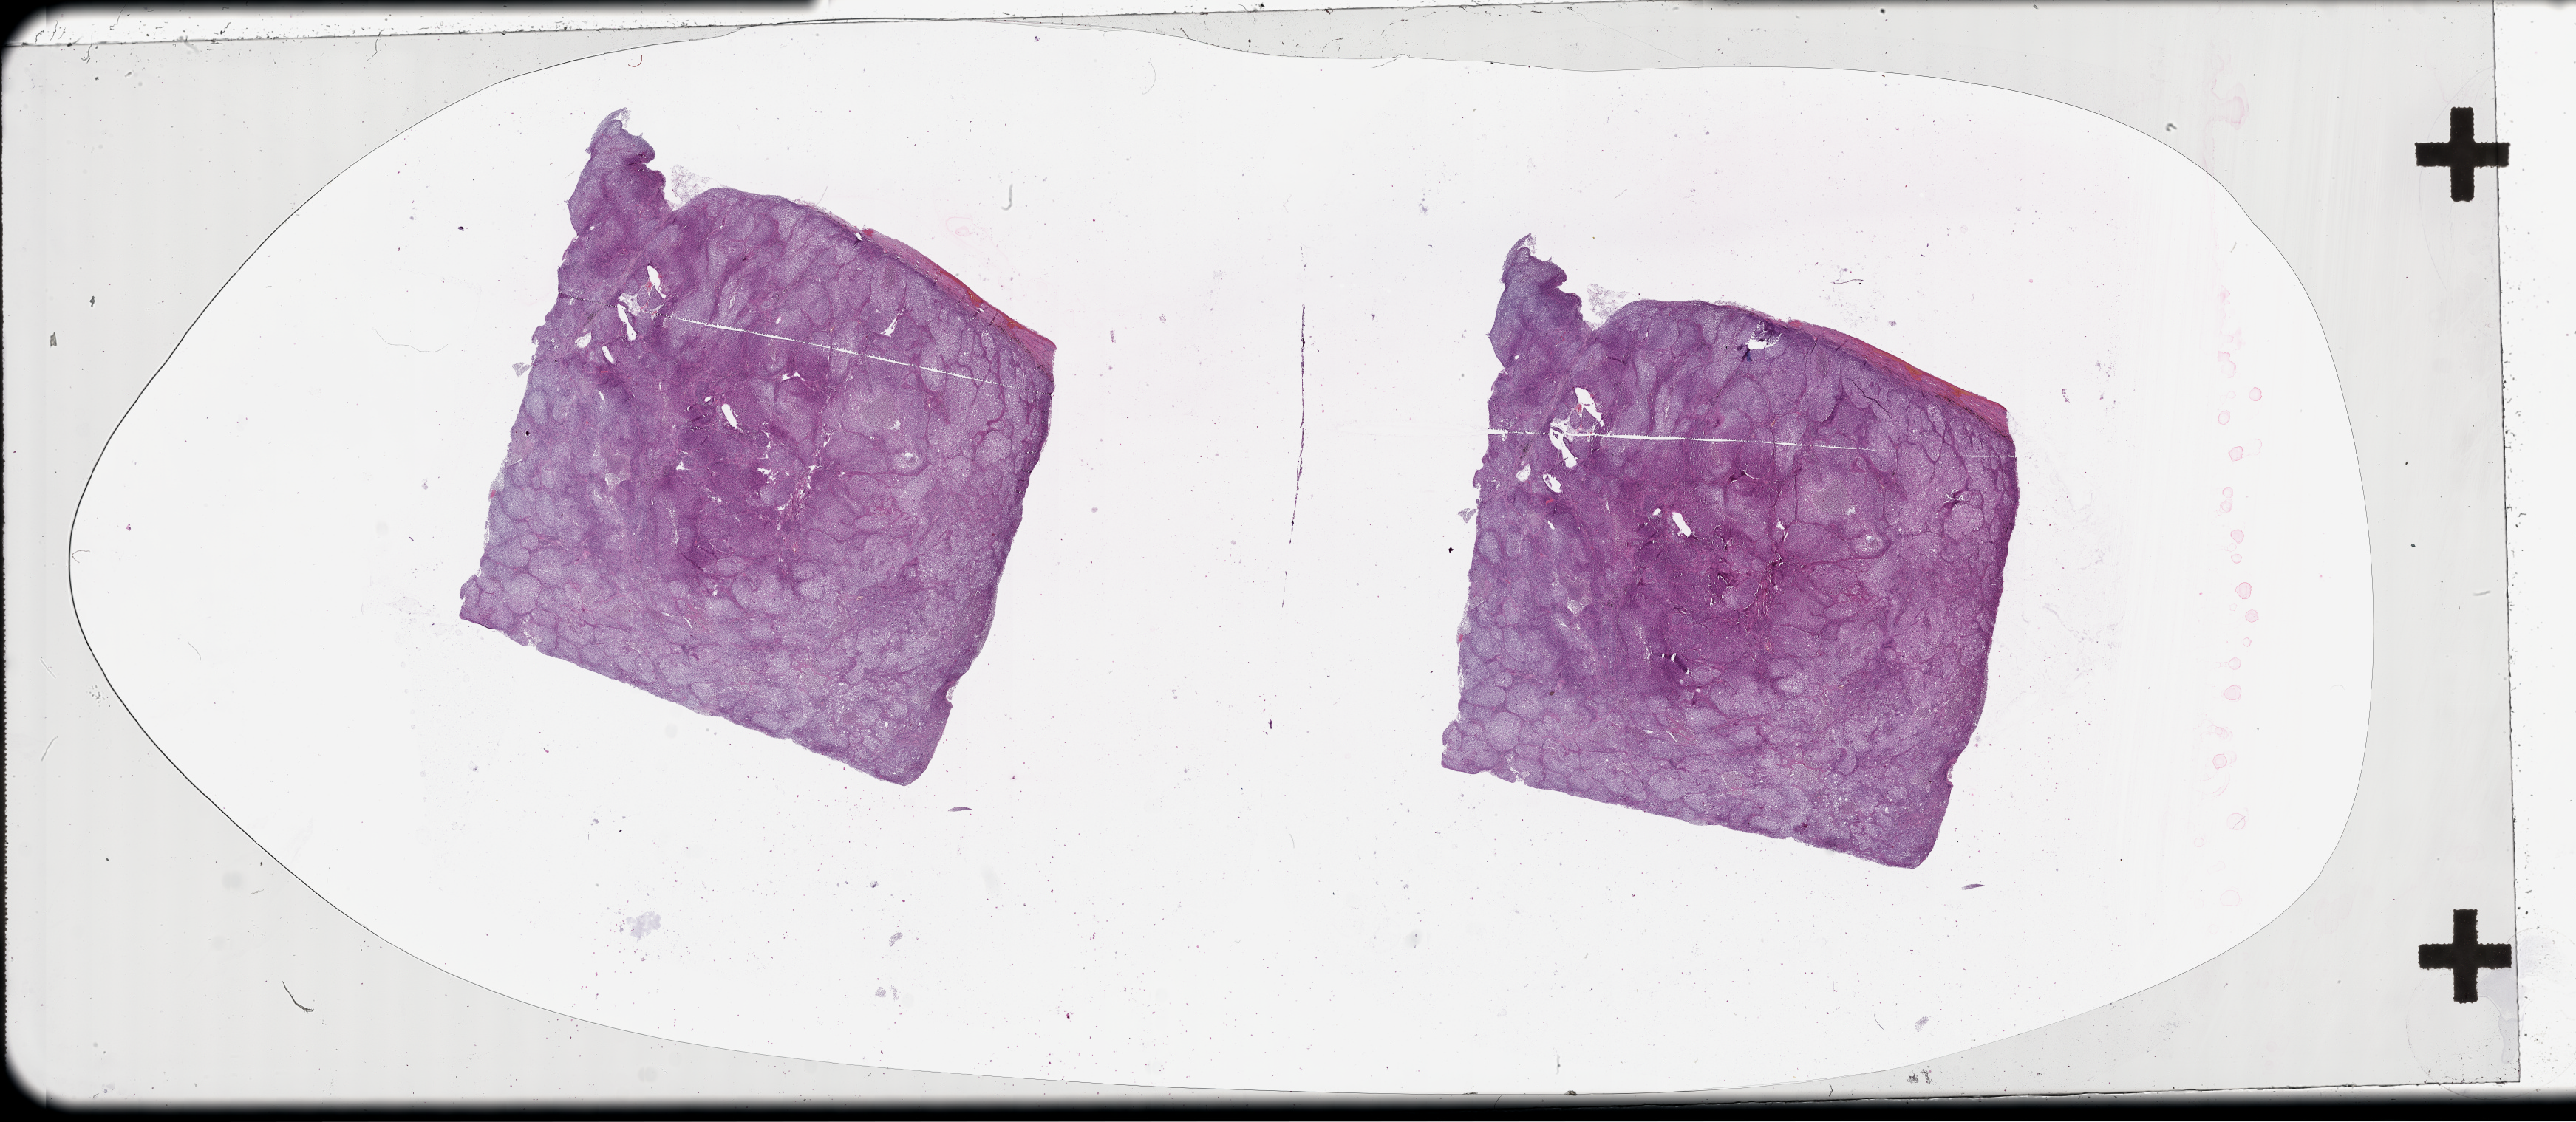
Whole-slide histology image, H&E-stained — whole scanned area (about 56.1 x 24.5 mm, acquisition: 20x scan) shown as a low-resolution overview. Tumour tissue sample, lung. 72-year-old female patient.
• patient diagnosis (cohort enrolment): squamous cell carcinoma (lung)